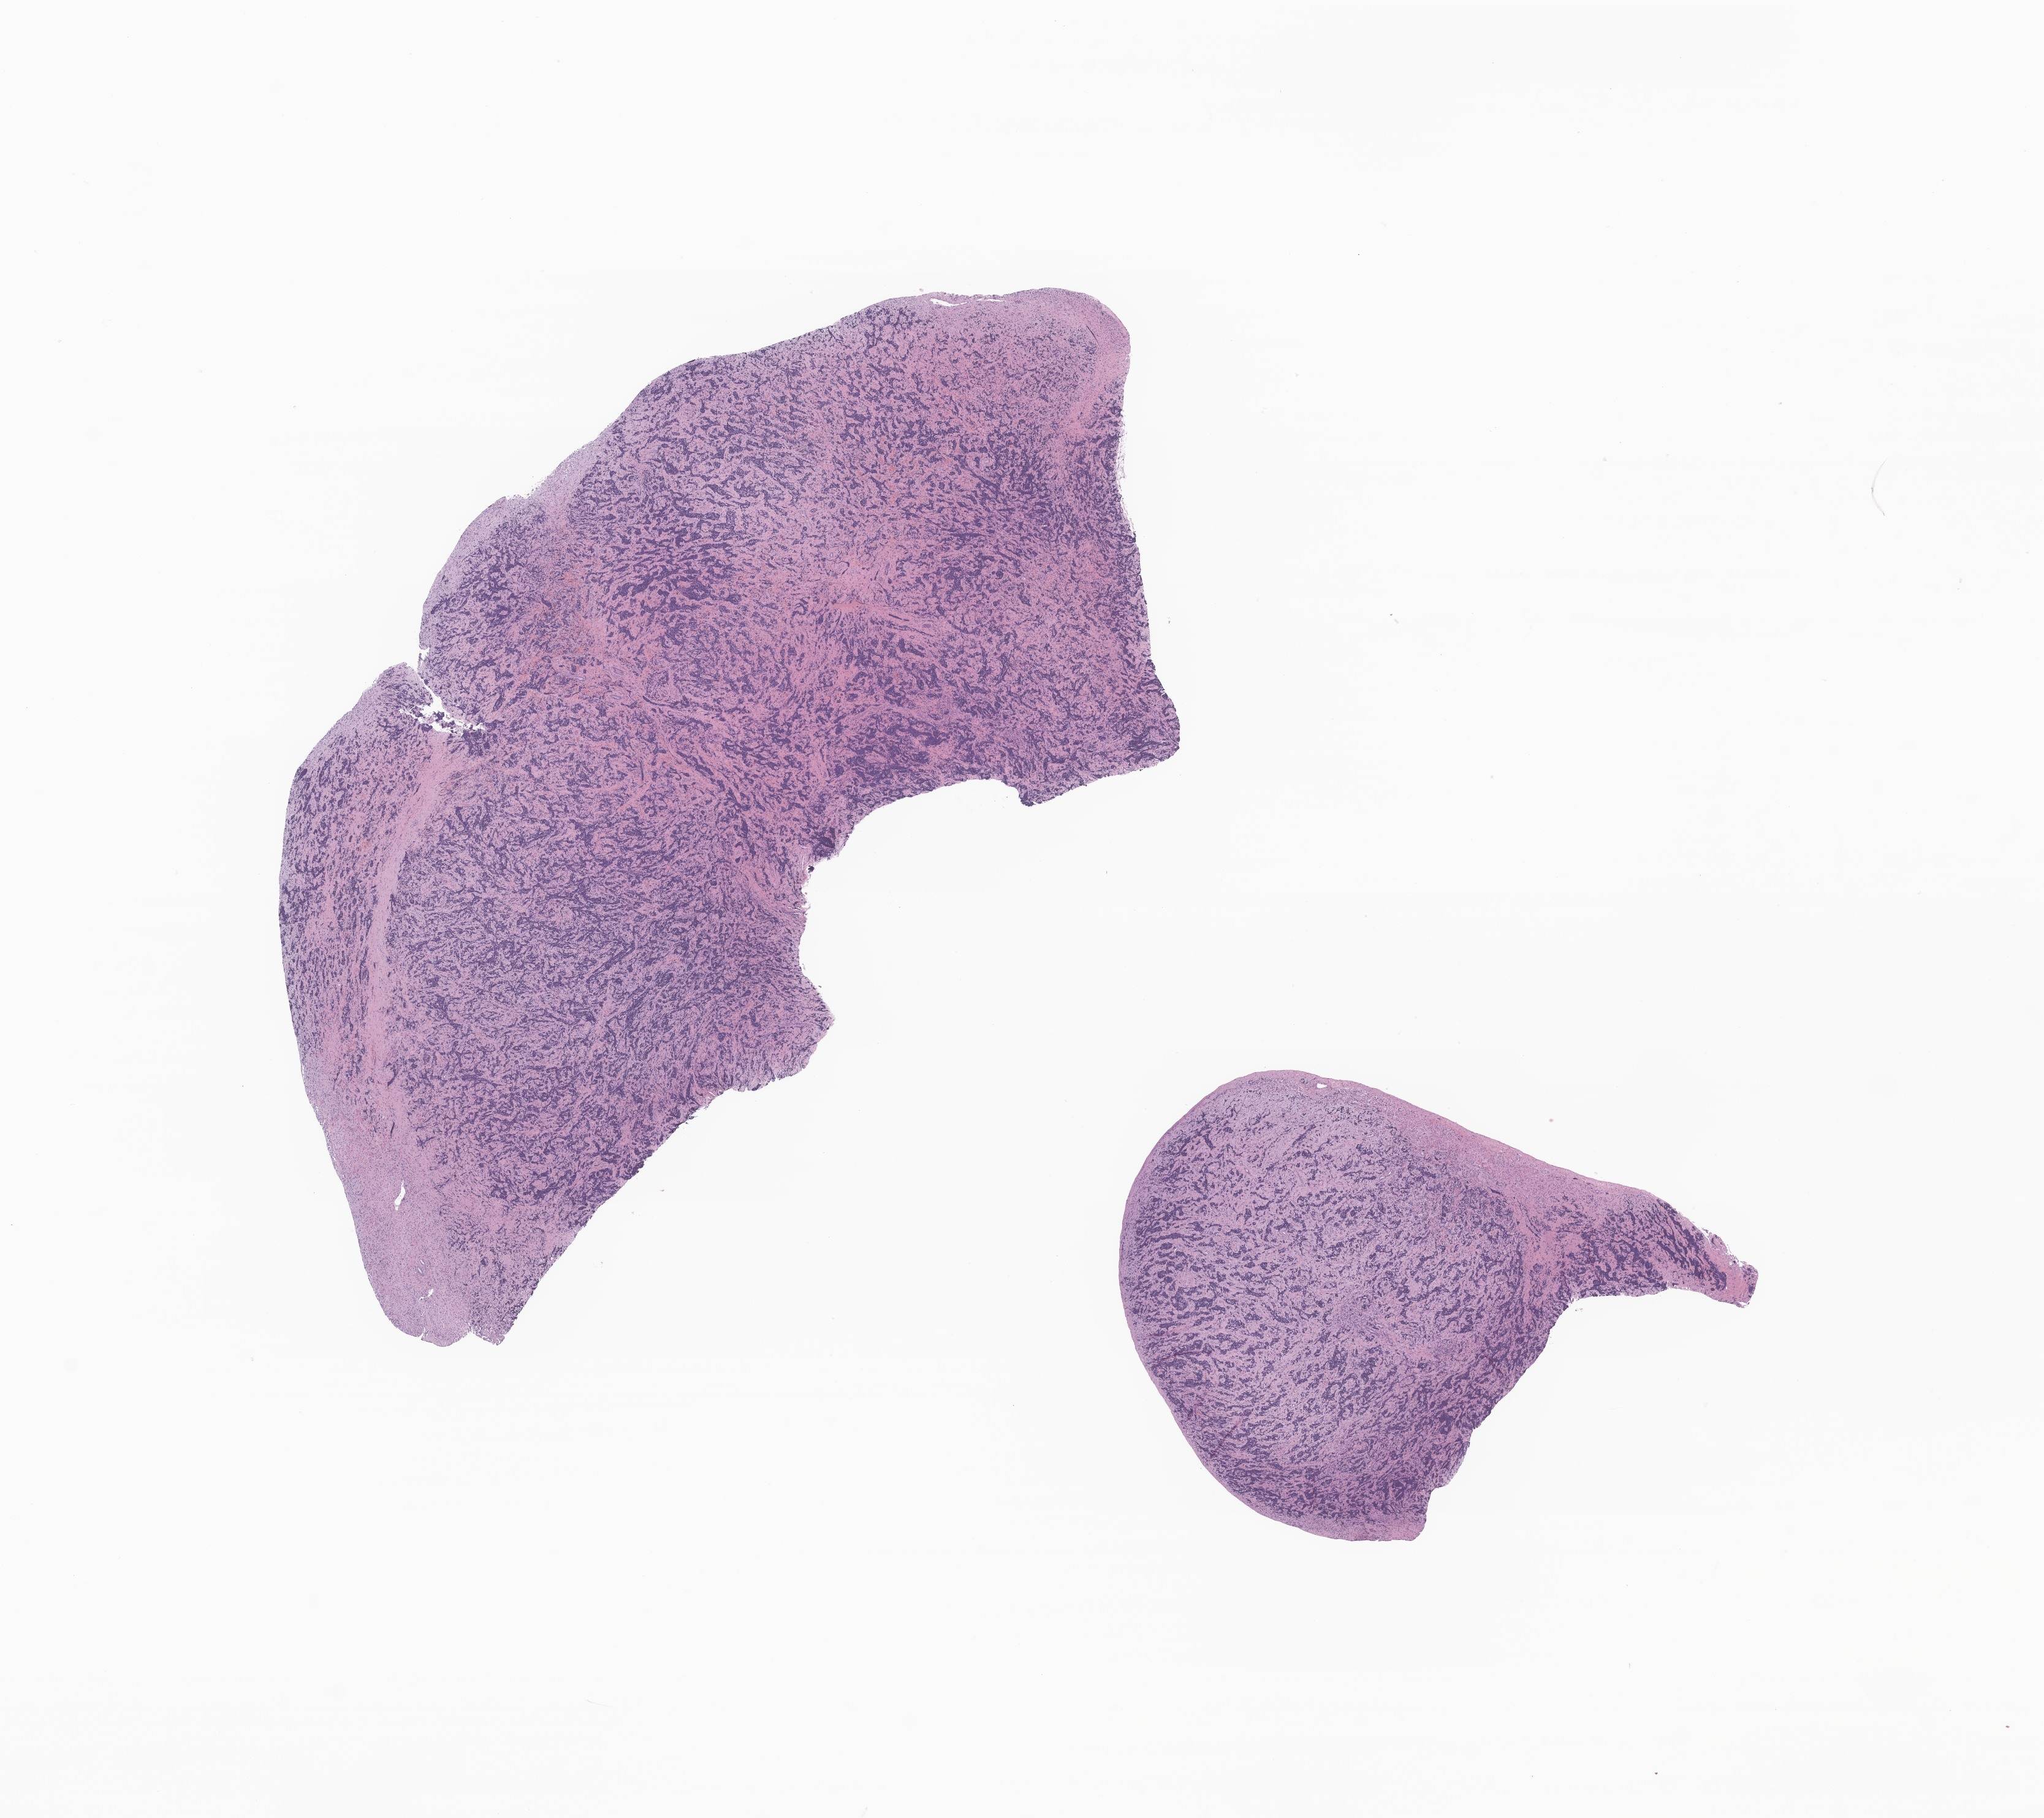
Haematoxylin and eosin whole-slide image of tumor tissue from the adrenal gland, a low-resolution overview of the entire scanned area, about 14.1 x 12.5 mm. Formalin-fixed, paraffin-embedded (FFPE) tissue. Female patient, age 130 days.
Recorded diagnosis: Neuroblastoma, NOS.